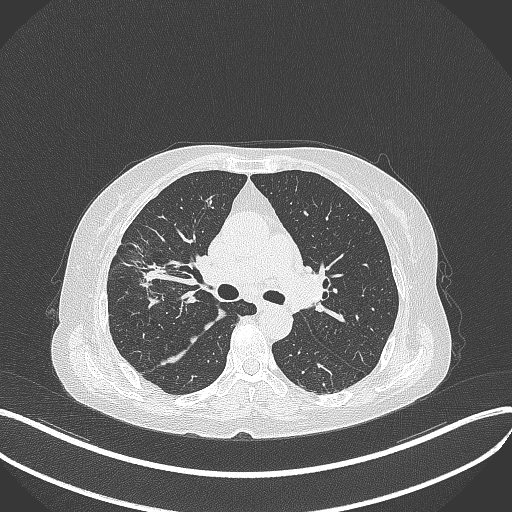
Chest CT, one axial slice; slice 248 of 429 in the series (ordered by position); reconstruction kernel B70f; 120 kVp; lung window (W 1500 / L -600 HU); 1 mm slice thickness; 512 × 512 image matrix, field of view 400 × 400 mm. Patient: female, 69 years. From the clinical record (not read from this slice): clinical TNM (as recorded): T1b N3 M0.
Structures marked on this image (rectangle marked by the reading radiologist):
- lung tumour (recorded histology: small cell carcinoma): bounding box (x1, y1, x2, y2) in pixels: (123, 253, 170, 289)